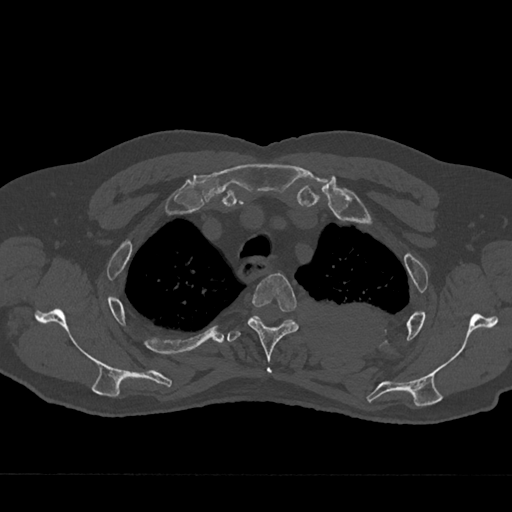
CT including the spine, one axial slice. Slice 560 of 797 in the series (ordered by position). Reconstruction kernel Br40s/3. 120 kVp. Bone window (W 1800 / L 400 HU). 0.5 mm slice thickness. 512 × 512 image matrix, field of view 377 × 377 mm. Patient: male, 75 years. Case-level facts recorded for this patient, not image findings: primary cancer: renal; vertebrae with lytic lesions (as recorded): T4.
Structures marked on this image (semi-automatically segmented with operator editing):
- T3 vertebra: box from (x=248, y=273) to (x=299, y=373) px
- T4 vertebra: (x=227, y=316)–(x=295, y=342)